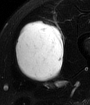
MRI of an extremity soft-tissue mass, one axial slice. Position 31 of 65 along the scan axis. T2-weighted fat-saturated. MR volume resampled by the dataset authors to the PET/CT grid (not the native acquisition matrix). 3.27 mm slice thickness. 90 × 105 image matrix. Male patient. Case-level facts recorded for this patient, not image findings: histological type: mixoid liposarcoma; grade: low; site of the primary tumour: left thigh.
Outlined on this slice (expert contour drawn on MRI and transferred to this co-registered scan by the dataset authors):
- gross tumour volume (mass): bounding box <14,21,65,81> (left, top, right, bottom; pixels)